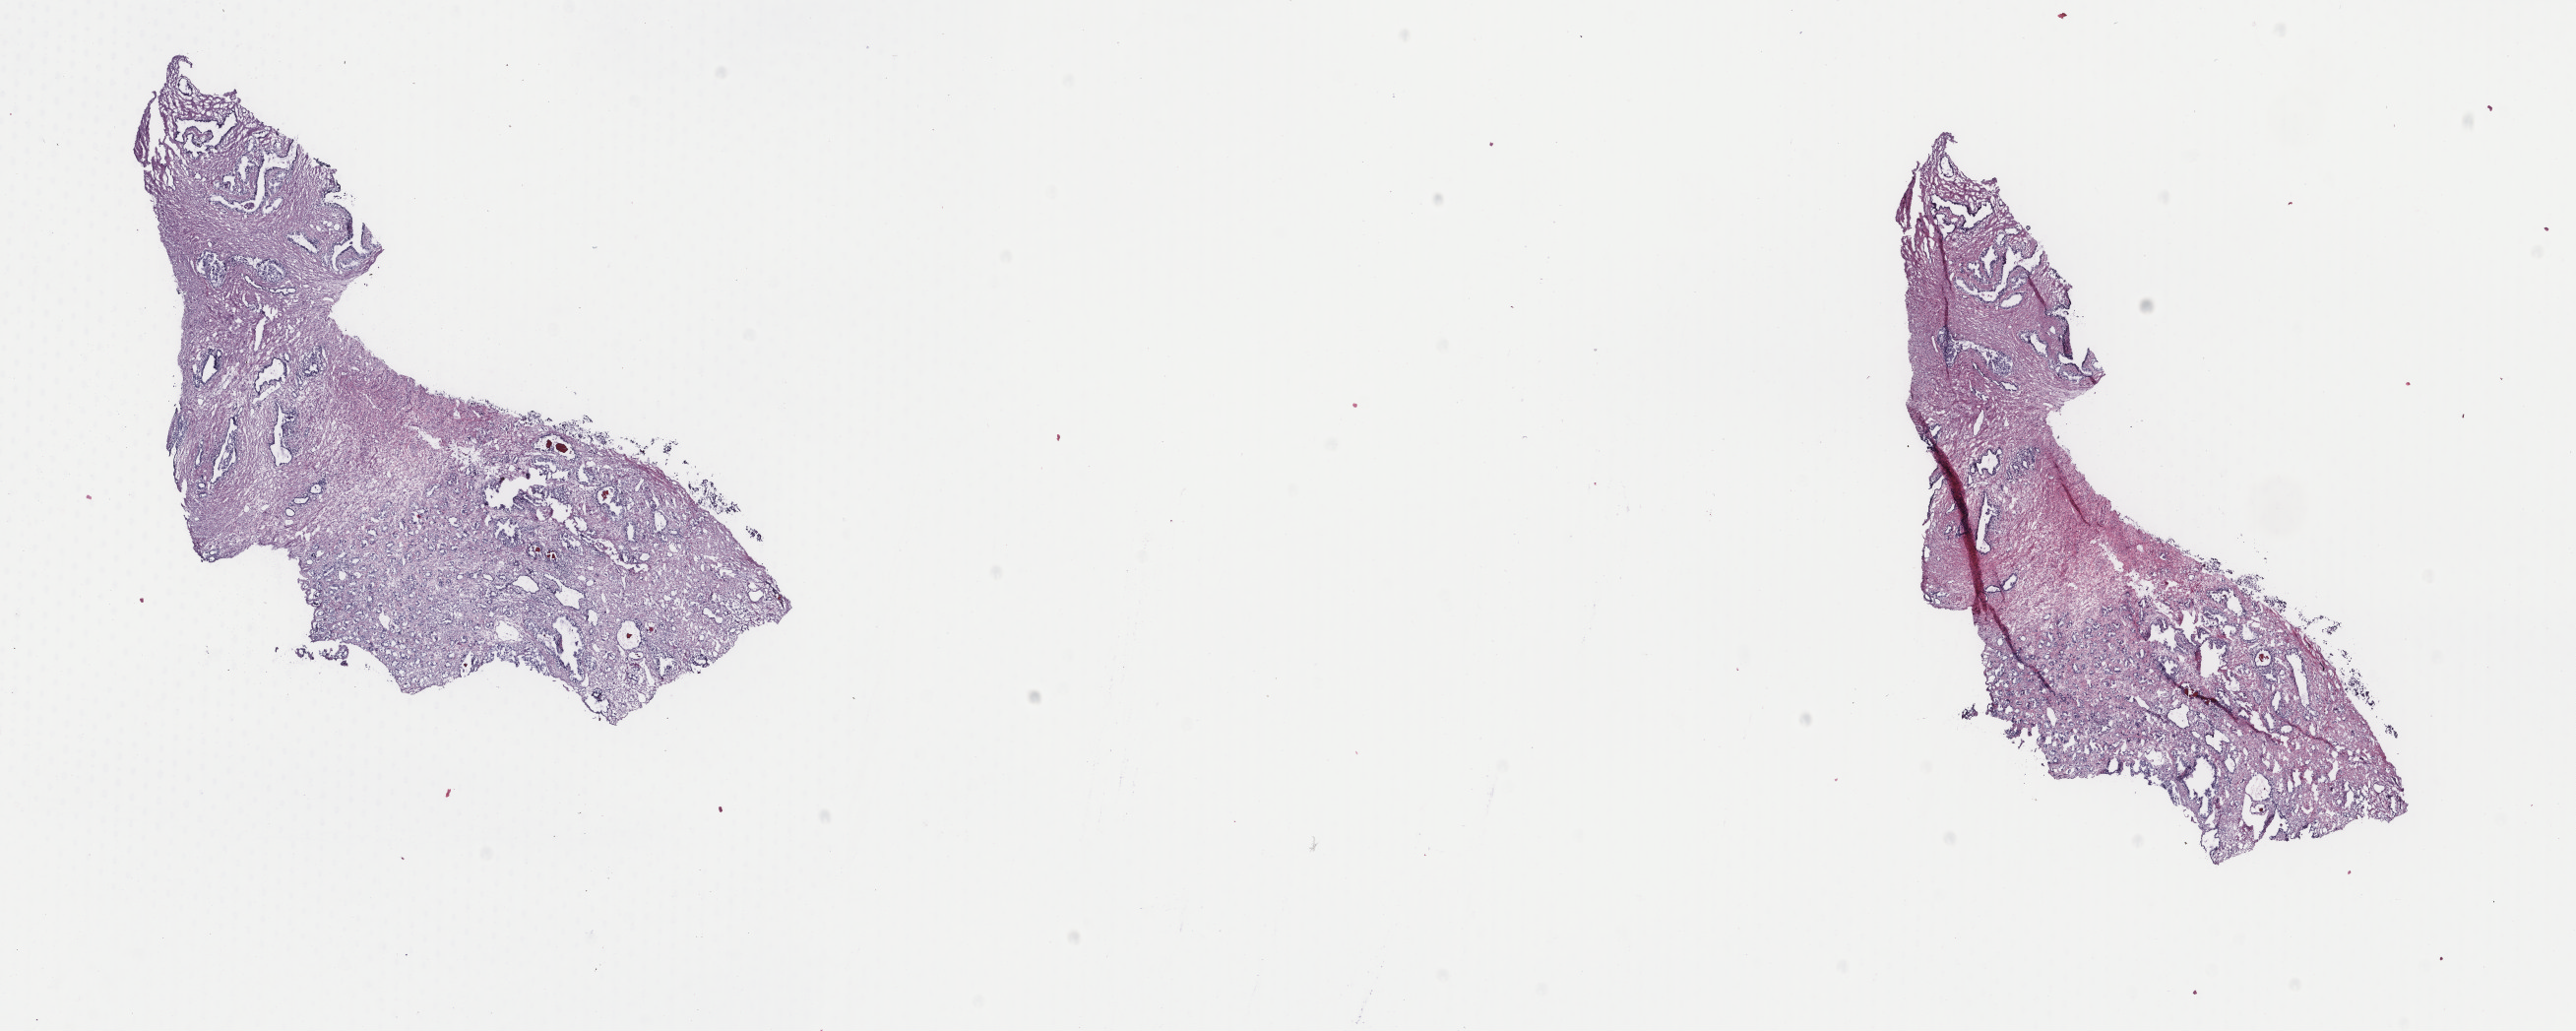
Digitized H&E tissue section (whole slide), low-resolution overview of the scanned area, about 20.8 x 8.3 mm; frozen section from the top of the tissue portion; sample: primary tumour, prostate. Patient: male, age at initial diagnosis 65 years. Gleason score: 7 (3+4). Slide review estimates, as recorded: tumour cells 40%, tumour nuclei 60%, normal cells 20%, stromal cells 40%, necrosis 0%. Inflammatory infiltration, as recorded: lymphocyte infiltration 0%, monocyte infiltration 0%, neutrophil infiltration 0%.
Pathologic diagnosis: Adenocarcinoma, NOS (prostate gland). Laterality: bilateral. Lymph nodes positive (case pathology): 0 of 4 examined.